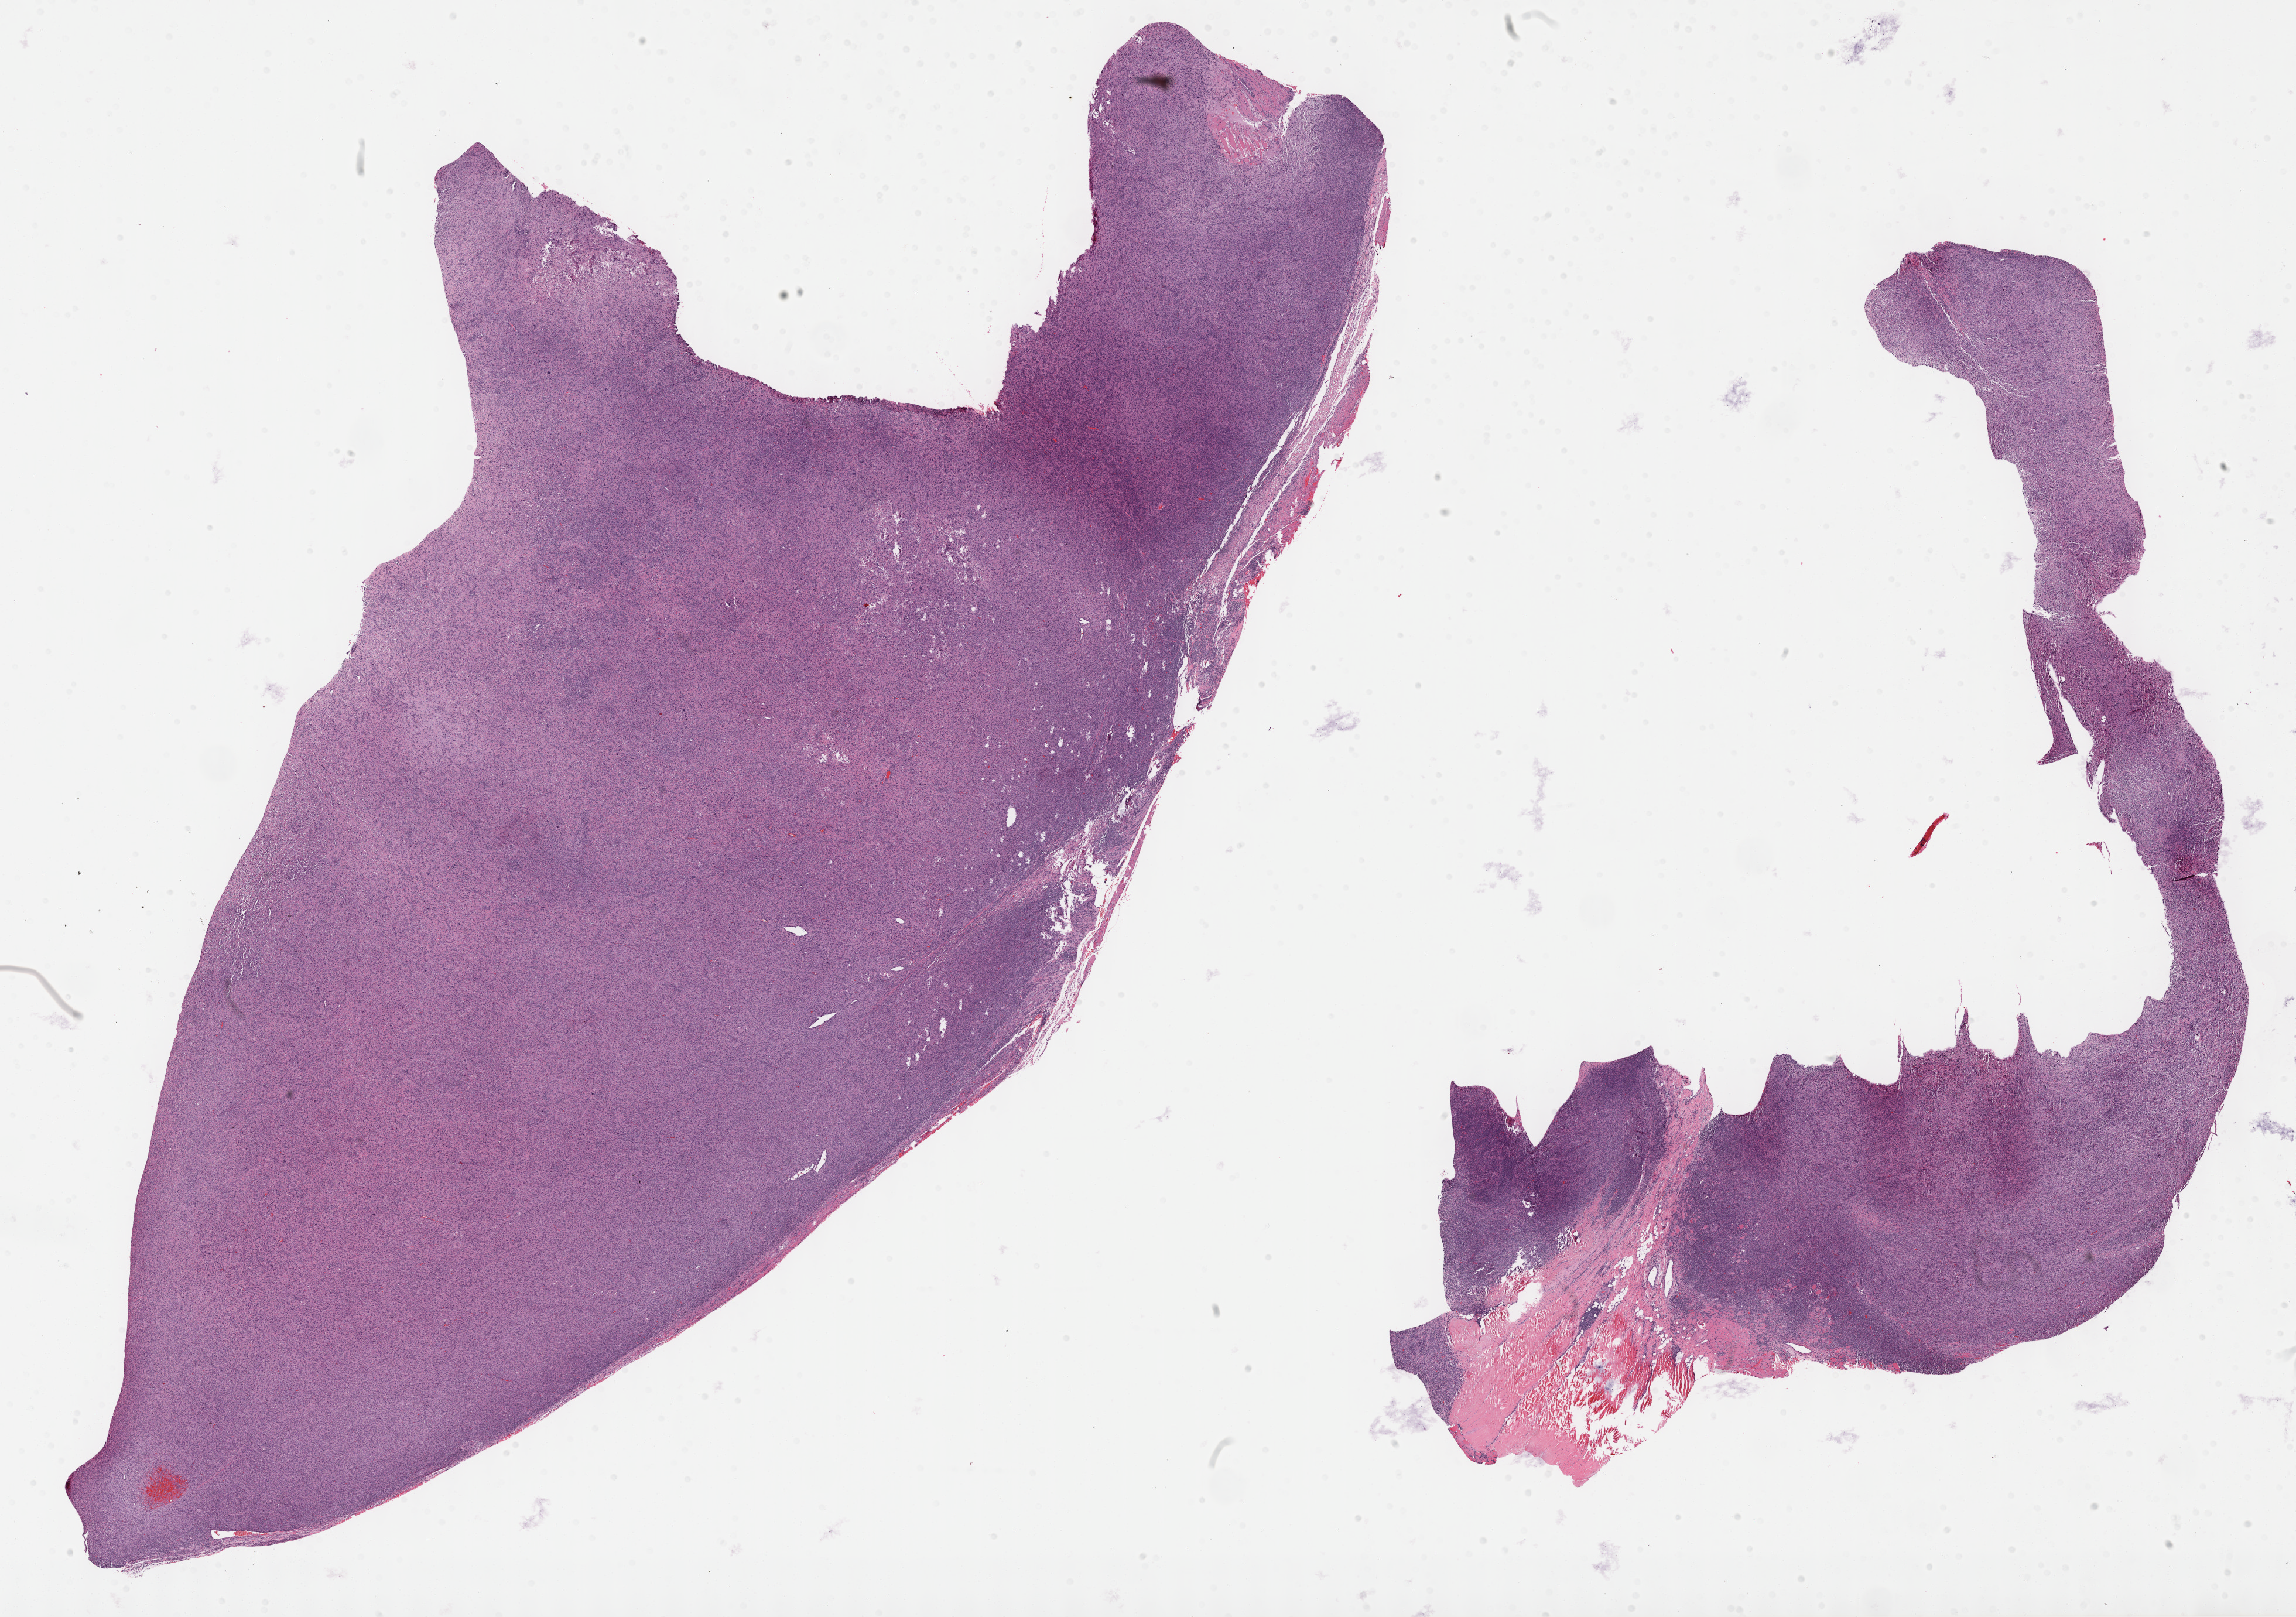
Whole-slide histology image, H&E — a low-resolution overview of the entire scanned area, about 31.7 x 22.3 mm (slide scanned at 40x), formalin-fixed paraffin-embedded (FFPE) diagnostic section, sample: primary tumour, connective, subcutaneous and other soft tissues. Female patient.
Diagnosis: Malignant fibrous histiocytoma (connective, subcutaneous and other soft tissues of trunk, NOS).